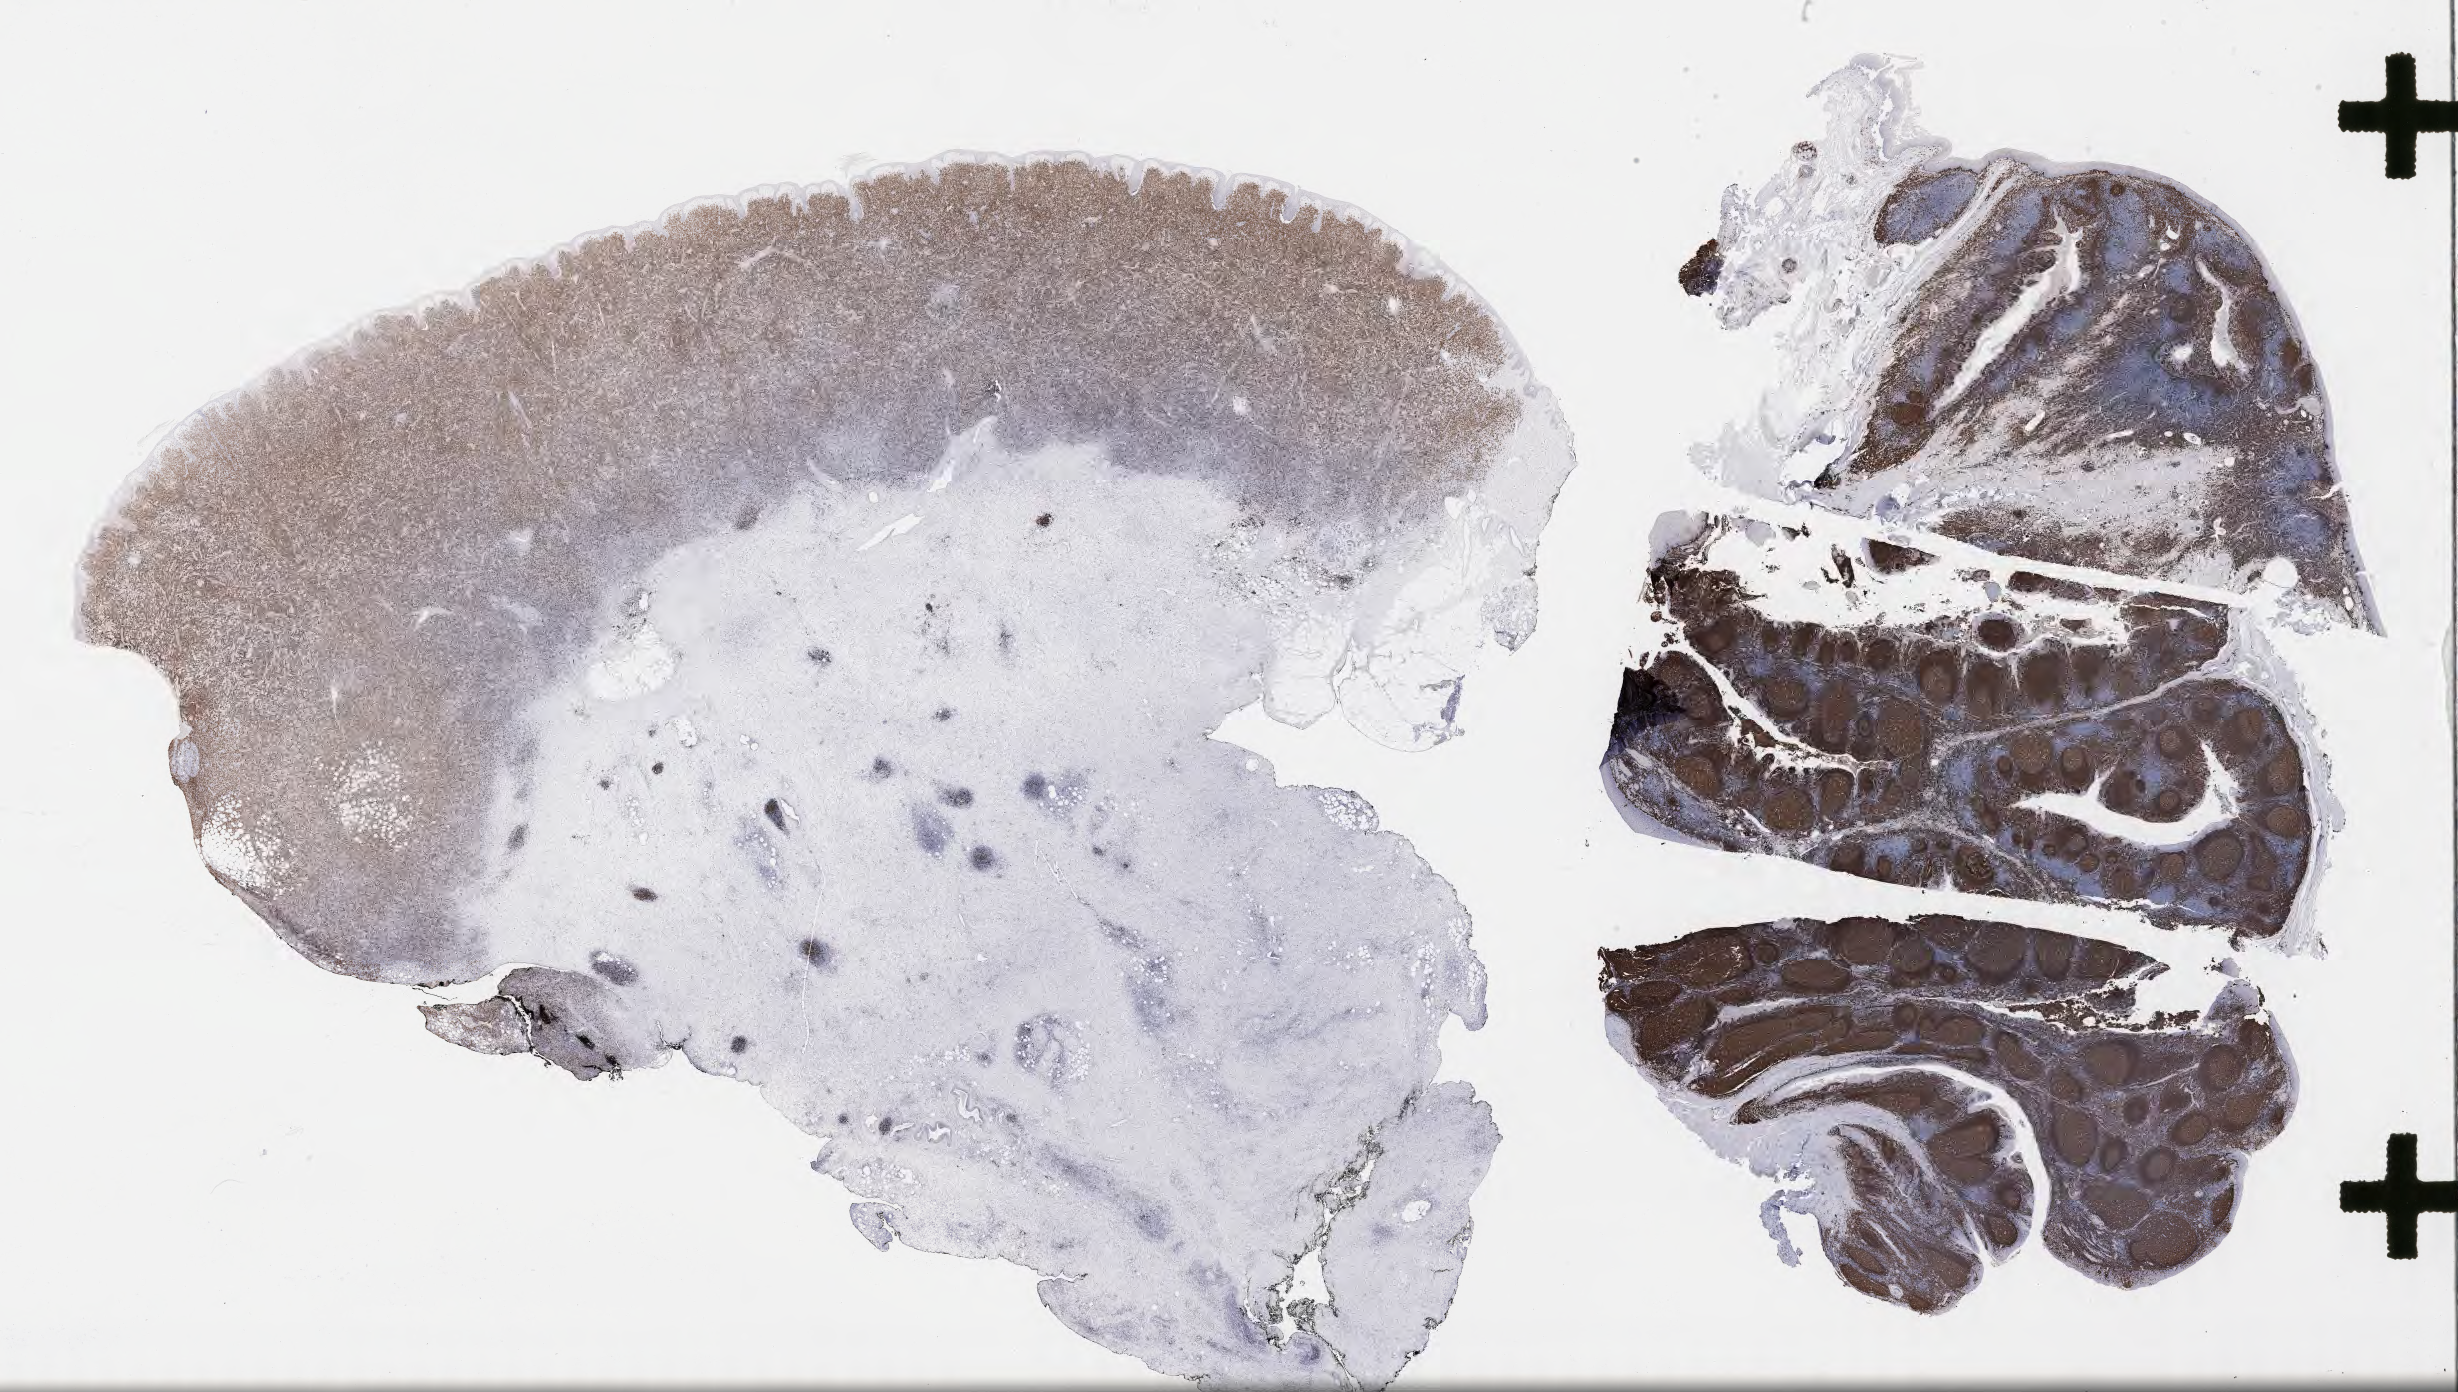
Immunohistochemistry (IHC) whole-slide image stained for CD79a — a low-resolution overview of the entire scanned area, about 39.7 x 22.5 mm, tumor tissue, site: lymph node. Patient male; aged 52.
• histologic diagnosis: Diffuse large B-cell lymphoma, NOS